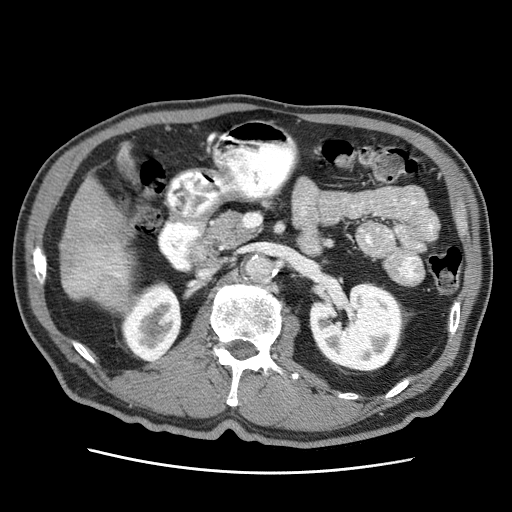
Contrast-enhanced abdominal CT (liver protocol), one axial slice; slice 11 of 75 in the series (ordered by position); reconstruction kernel STANDARD; 120 kVp; soft-tissue window (W 400 / L 40 HU); 2.5 mm slice thickness; 512 × 512 image matrix, field of view 360 × 360 mm. Case-level facts recorded for this patient, not image findings: diagnosis: hepatocellular carcinoma (patient treated with transarterial chemoembolisation; whether this scan precedes or follows treatment is not stated here); TNM stage (as recorded): Stage-IIIA; Child-Pugh class: A; tumour differentiation: well differentiated; tumour nodularity: multinodular.
Structures marked on this image (semi-automatic segmentation, software-assisted and operator-edited):
- liver parenchyma outside the tumour (the mass and vessels are separate outlines, so this box may not span the whole liver): box from (x=60, y=178) to (x=130, y=310) px
- mass: (x=60, y=180)–(x=127, y=278)
- liver vessels: (x=84, y=266)–(x=121, y=278)